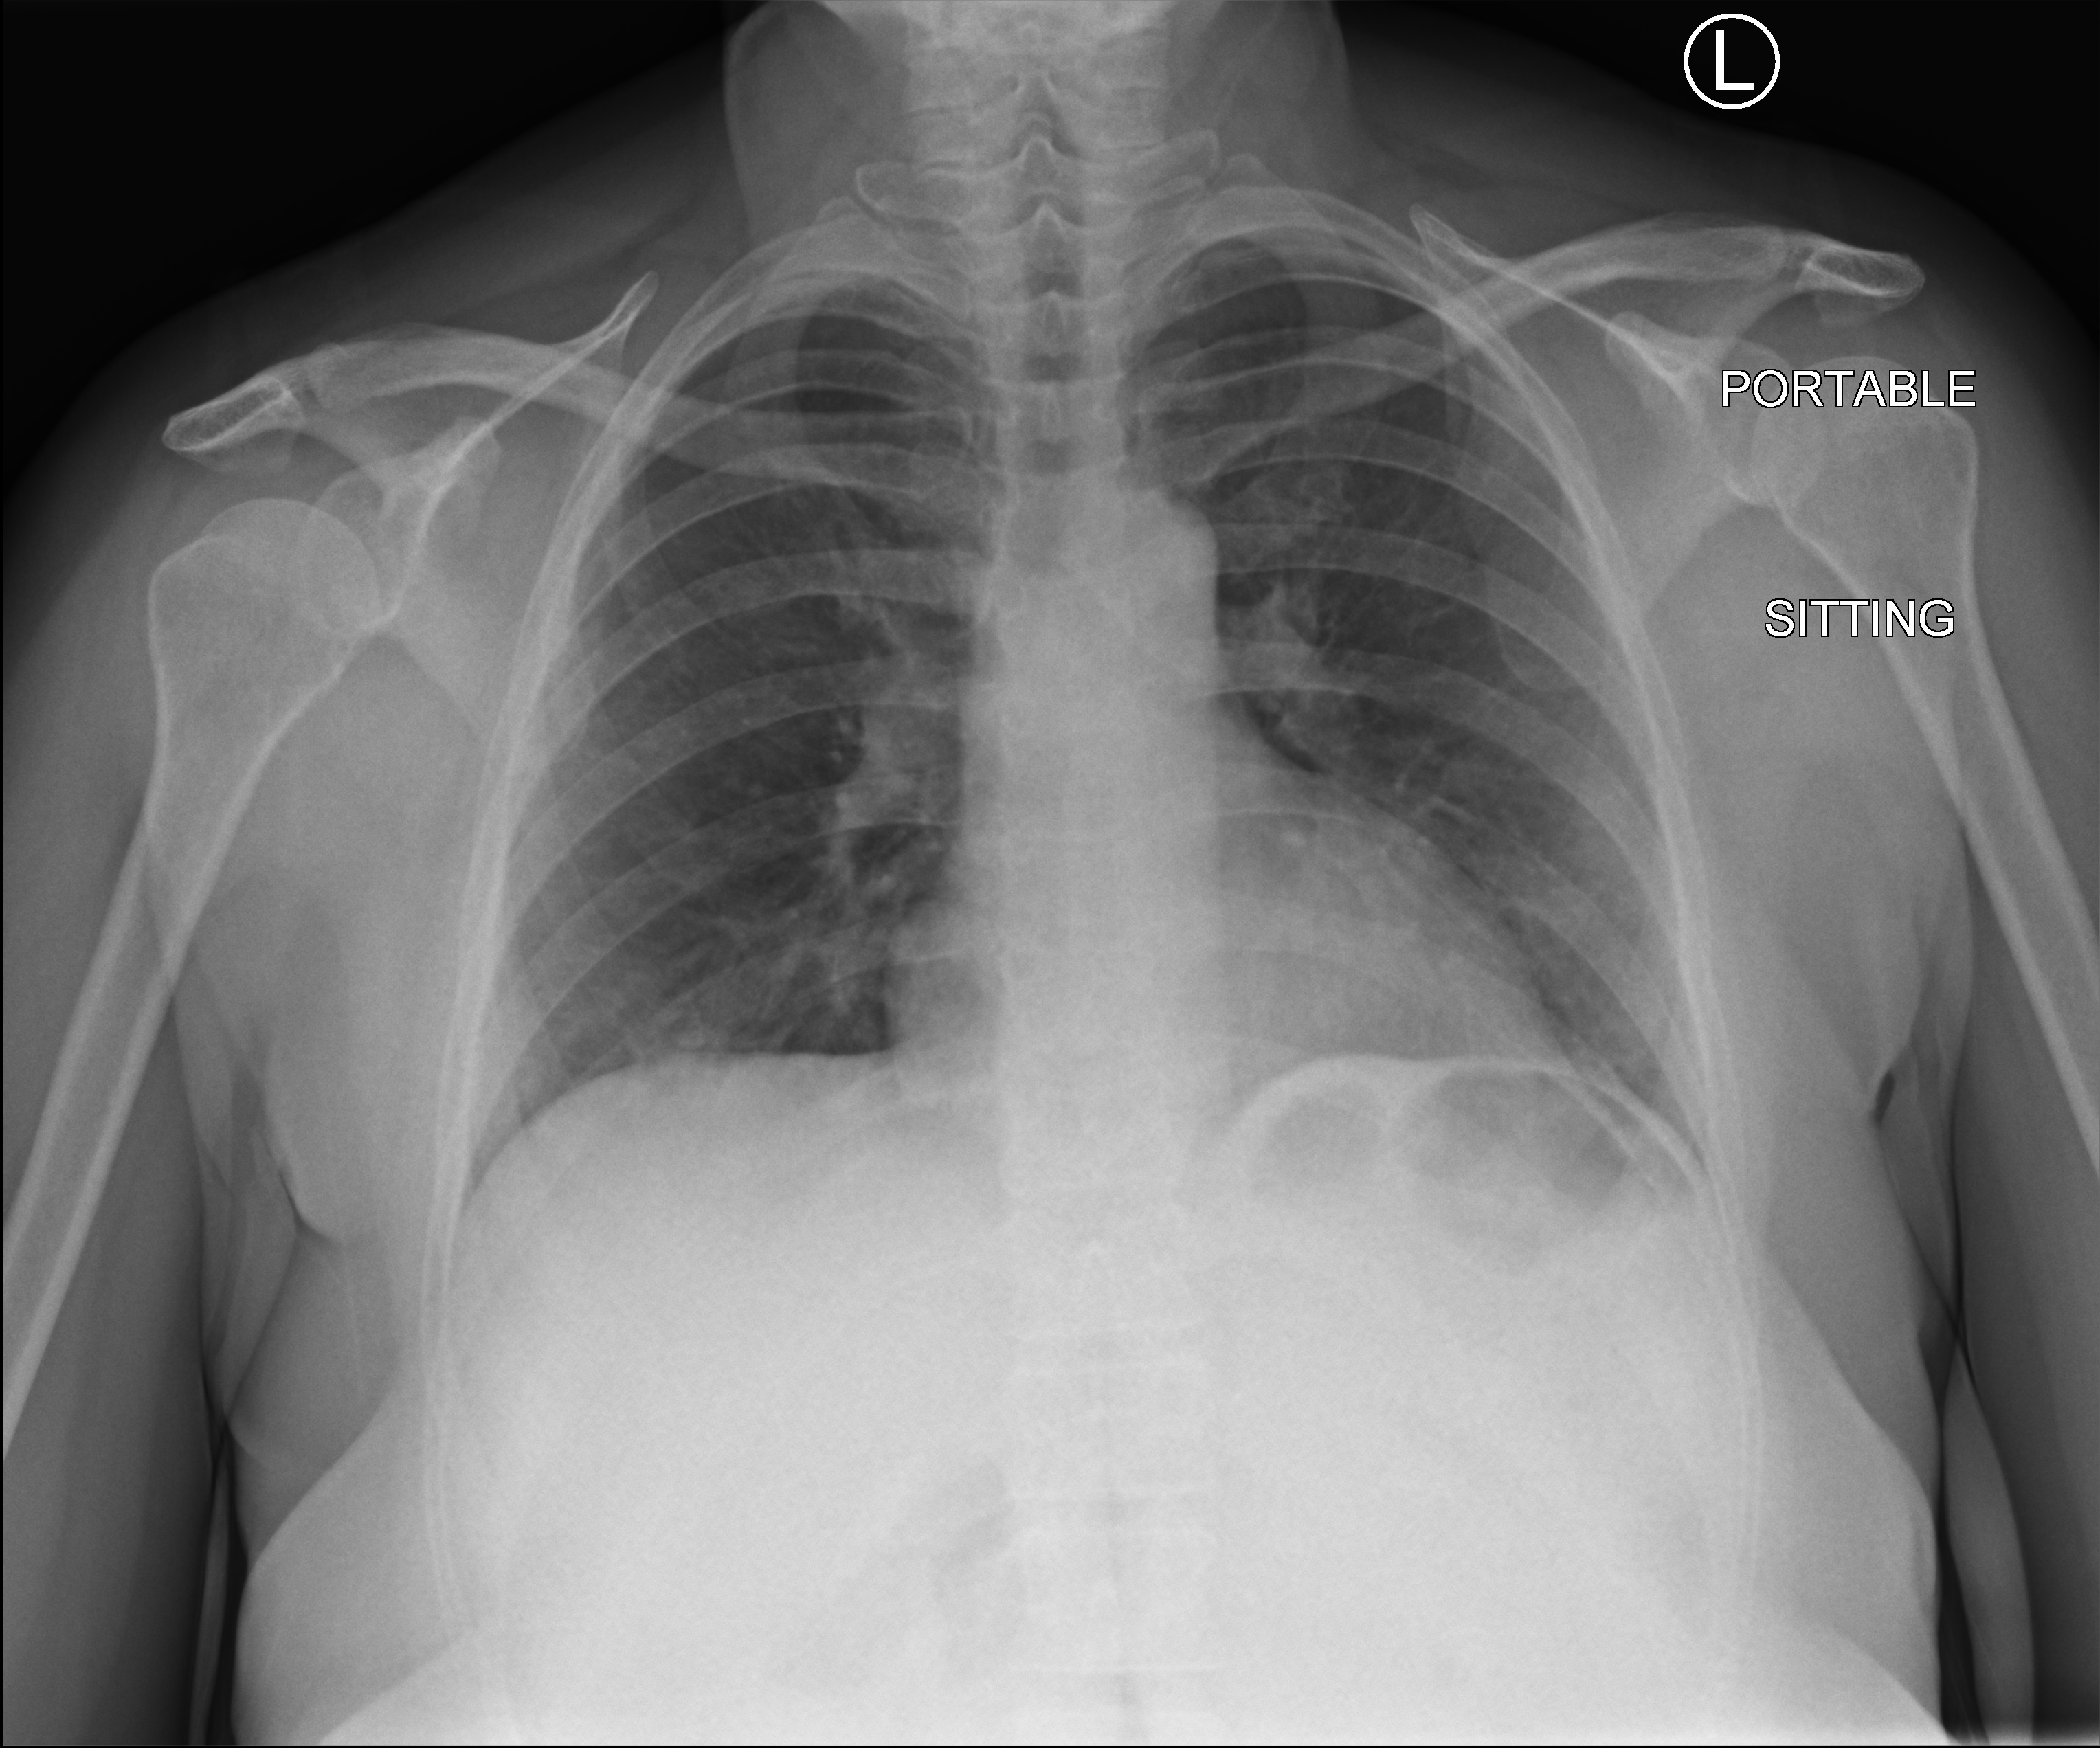
Chest X-ray (portable), anteroposterior (AP) projection. Female patient hospitalised with COVID-19, age 18–59 years.
Hospital-stay facts (about this admission, not read from this image; timing relative to this image not recorded):
- diabetes (admission record): no
- chronic kidney disease (admission record): no